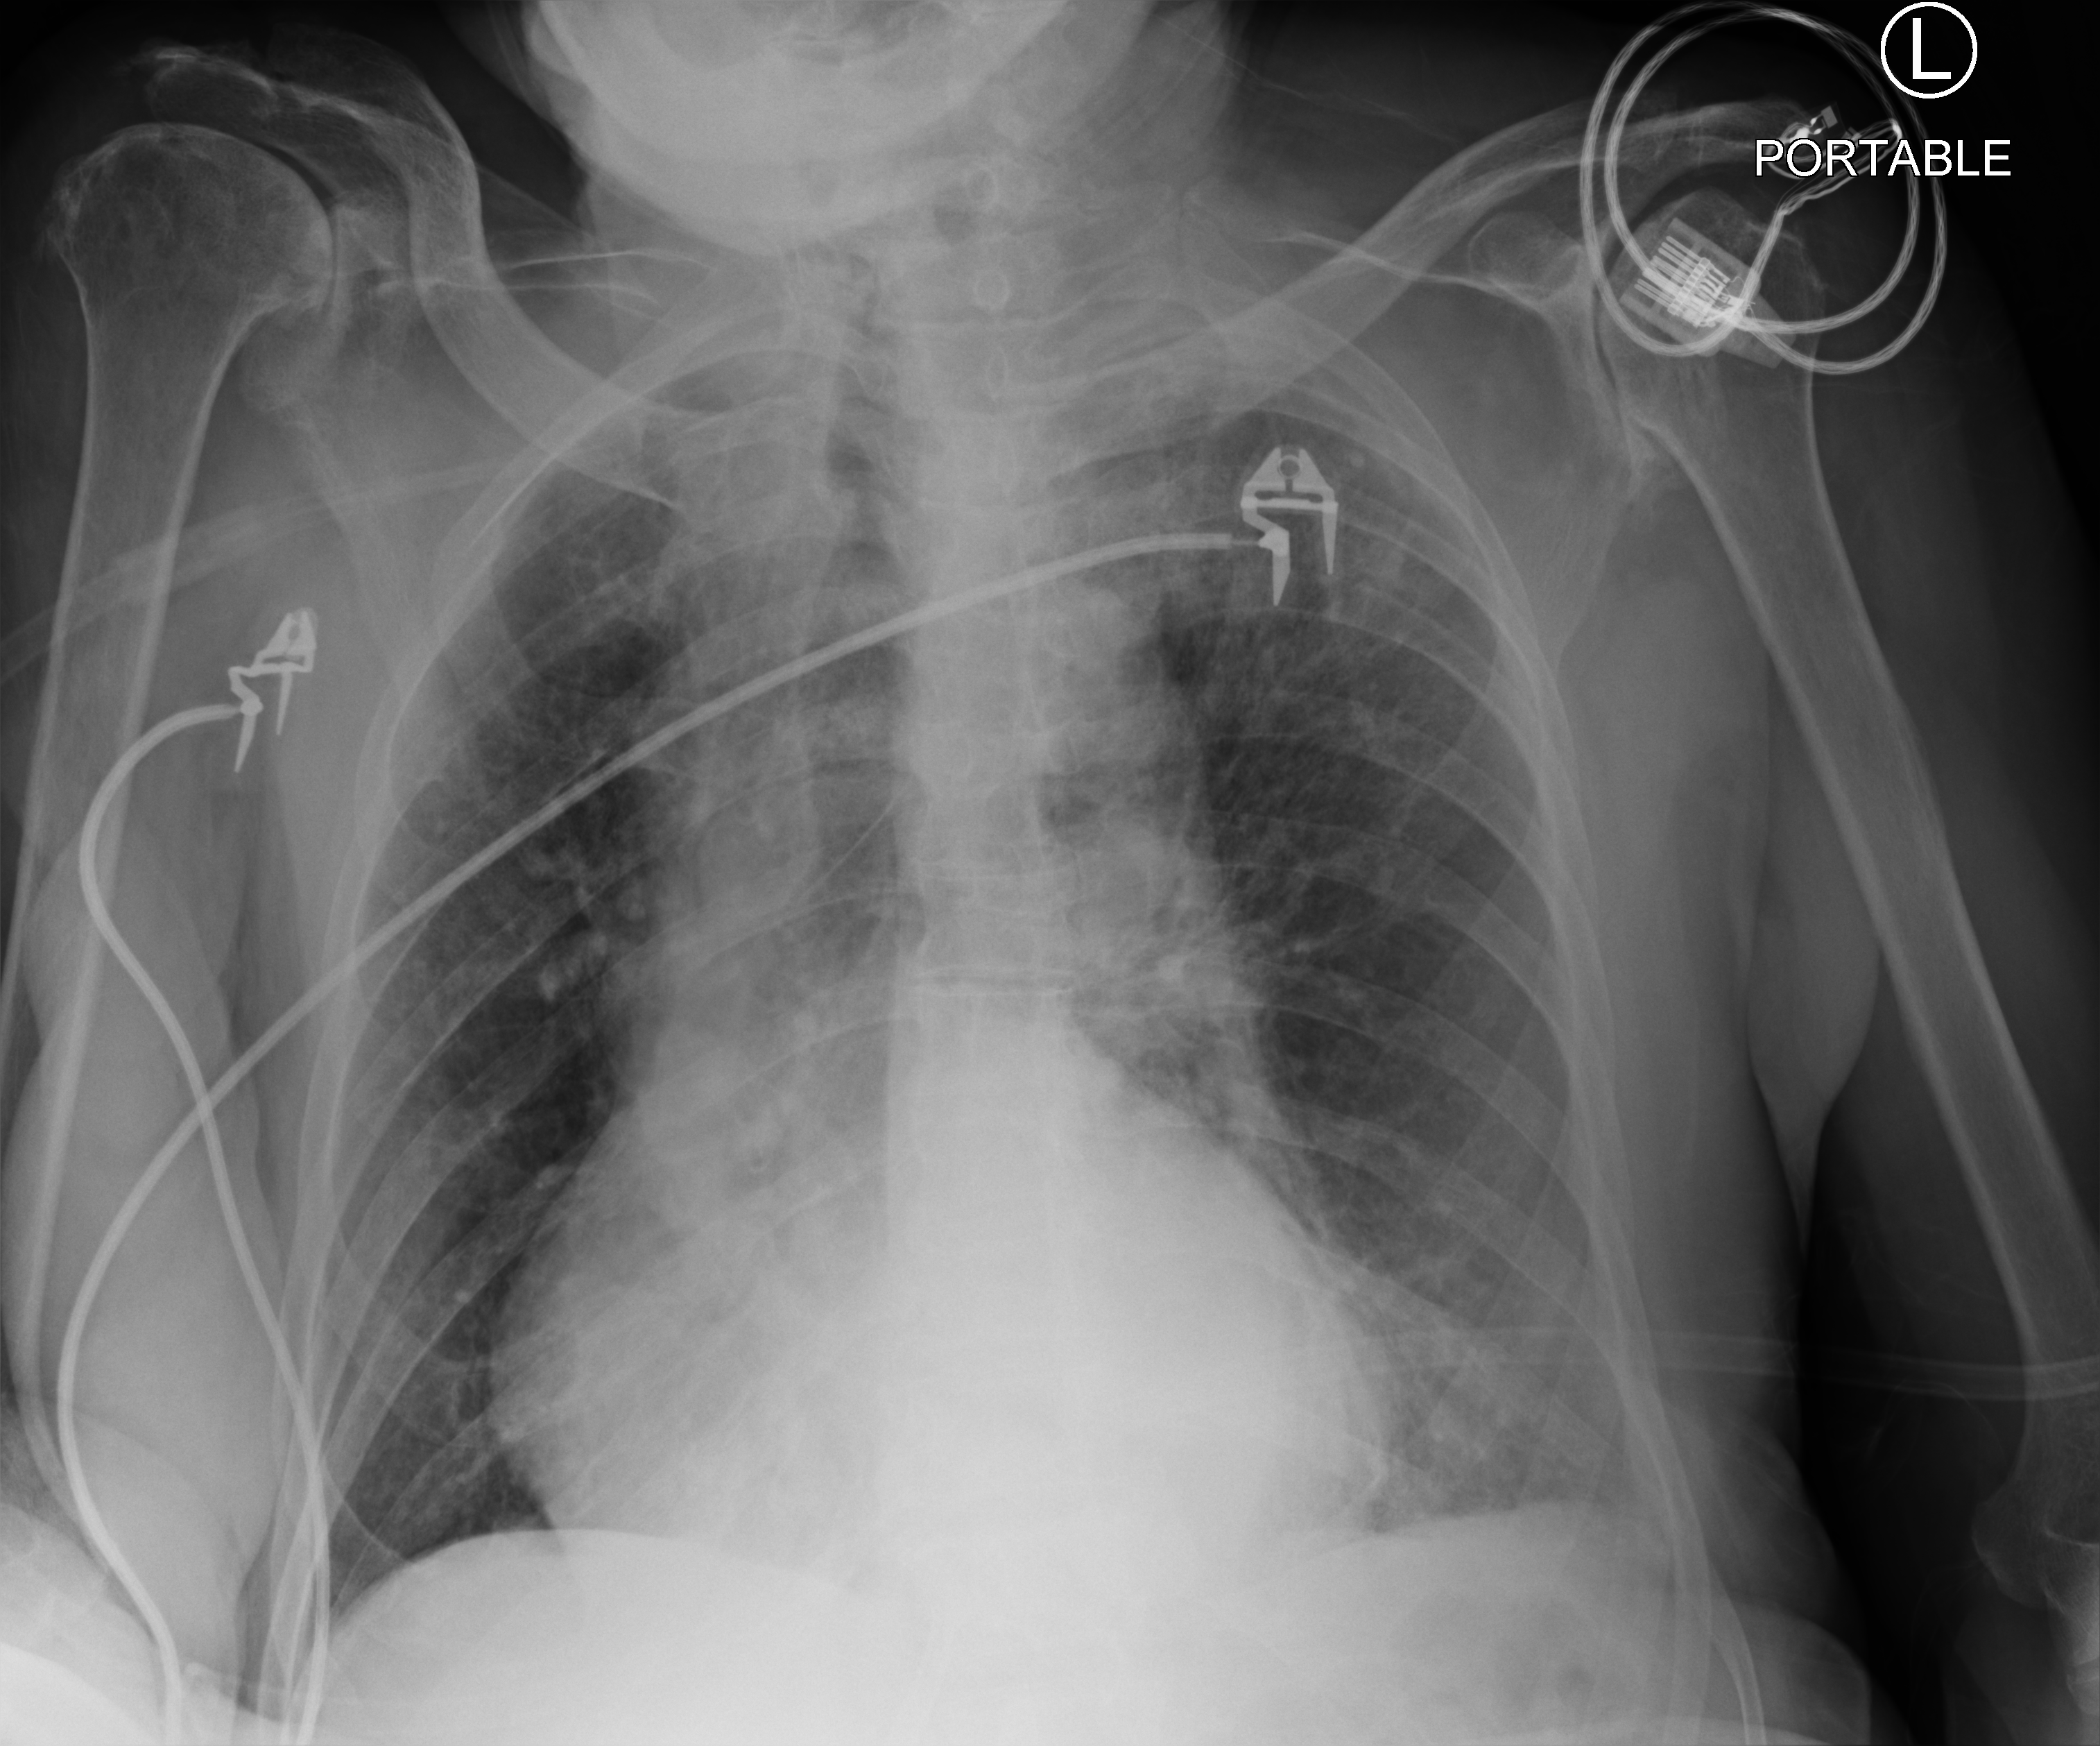
Bedside chest radiograph (computed radiography); anteroposterior (AP) projection. Patient hospitalised with COVID-19; male, aged 75–90 years.
From the hospital-stay record, not from the radiograph (when in the stay this image was taken is not recorded): other chronic lung disease (admission record): no.